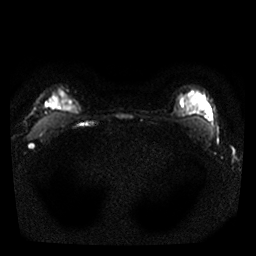
Breast MRI, one axial slice. Position 22 of 25 along the scan axis. Diffusion-weighted series; image 2 of 4 stored at this slice position (different b-values; order by instance number). 1.5 T. 4 mm slice thickness. 256 × 256 image matrix, field of view 290 × 290 mm. Female patient.
Outlined on this slice (outlined manually by an expert reader):
- tumour on diffusion-weighted imaging: bounding box <48,96,77,114> (left, top, right, bottom; pixels)